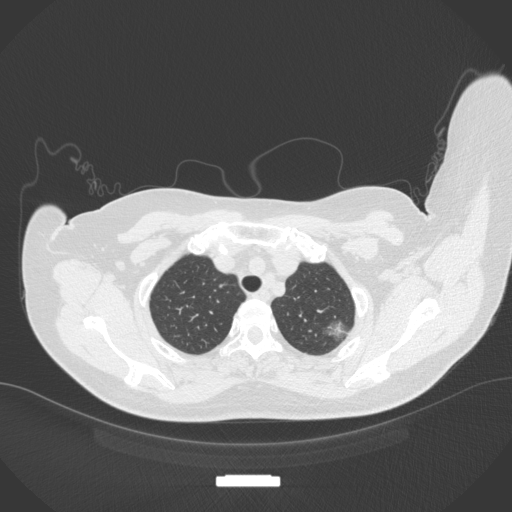
Chest CT, one axial slice; slice 314 of 386 in the series (ordered by position); reconstruction kernel B31f; 120 kVp; lung window (W 1500 / L -600 HU); 512 × 512 image matrix, field of view 400 × 400 mm. Female patient, age 58 years. From the clinical record (not read from this slice): clinical TNM (as recorded): T1c N0 M0.
Outlined on this slice (rectangle marked by the reading radiologist):
- lung tumour (recorded histology: adenocarcinoma): bounding box <322,318,348,340> (left, top, right, bottom; pixels)